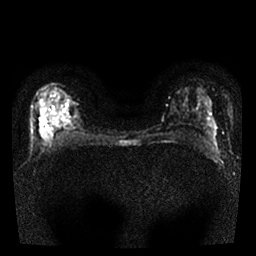
Breast MRI, one axial slice. Position 16 of 25 along the scan axis. Diffusion-weighted series; image 2 of 4 stored at this slice position (different b-values; order by instance number). 1.5 T. 4 mm slice thickness. 256 × 256 image matrix, field of view 300 × 300 mm. Female patient.
Structures marked on this image (manually delineated by an expert):
- tumour on diffusion-weighted imaging: bounding box <40,118,46,131> (left, top, right, bottom; pixels)